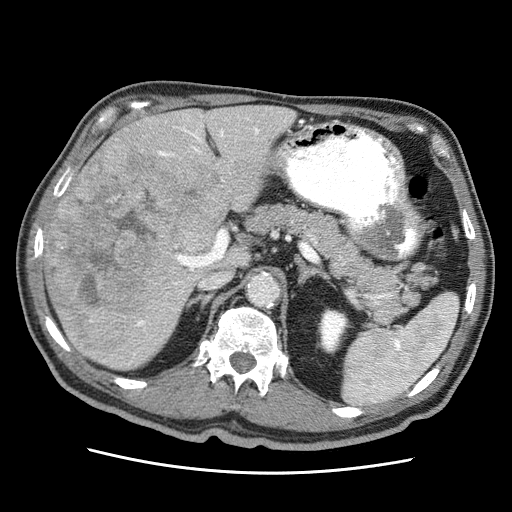
Contrast-enhanced abdominal CT (liver protocol), one axial slice; slice 28 of 75 in the series (ordered by position); reconstruction kernel STANDARD; soft-tissue window (W 400 / L 40 HU); 2.5 mm slice thickness; 512 × 512 image matrix, field of view 360 × 360 mm. Case-level facts recorded for this patient, not image findings: diagnosis: hepatocellular carcinoma (patient treated with transarterial chemoembolisation; whether this scan precedes or follows treatment is not stated here); TNM stage (as recorded): Stage-IIIA; Child-Pugh class: A; tumour differentiation: well differentiated; tumour size: 13.9 cm.
Structures marked on this image (semi-automatically segmented with operator editing):
- liver parenchyma outside the tumour (the mass and vessels are separate outlines, so this box may not span the whole liver): box from (x=44, y=106) to (x=295, y=370) px
- mass: (x=48, y=137)–(x=219, y=365)
- liver vessels: (x=130, y=115)–(x=287, y=363)